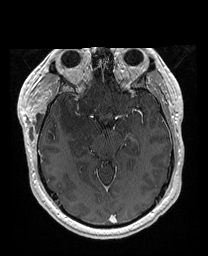
Brain MRI from a brain-tumour surgery series, one axial slice; position 109 of 176 along the scan axis; T1-weighted post-contrast; 1 mm slice thickness; 208 × 256 image matrix. Case-level facts recorded for this patient, not image findings: histopathology: Astrocytoma; WHO grade: 4; IDH mutation: yes.
Annotated regions visible in this slice (expert manual segmentation):
- previous resection cavity: box from (x=56, y=62) to (x=64, y=72) px